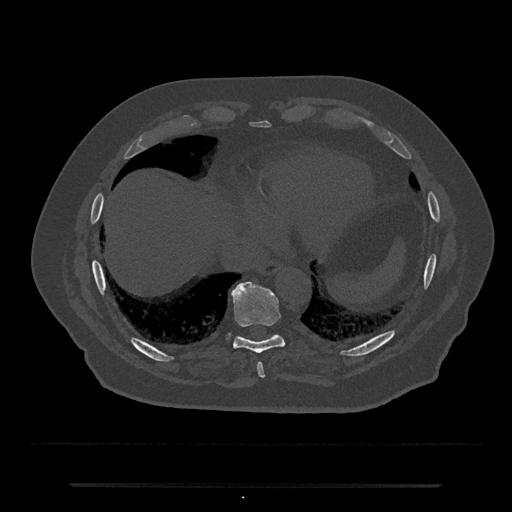
CT including the spine, one axial slice; position 752 of 797 along the scan axis; 120 kVp; bone window (W 1800 / L 400 HU); 0.5 mm slice thickness; 512 × 512 image matrix. Male patient, age 80 years. From the clinical record (not read from this slice): primary cancer: prostate; vertebrae with lytic lesions (as recorded): L1, T11.
Structures marked on this image (semi-automatically segmented with operator editing):
- T10 vertebra: box from (x=238, y=333) to (x=278, y=338) px
- T8 vertebra: (x=257, y=363)–(x=265, y=378)
- T9 vertebra: (x=230, y=281)–(x=284, y=354)